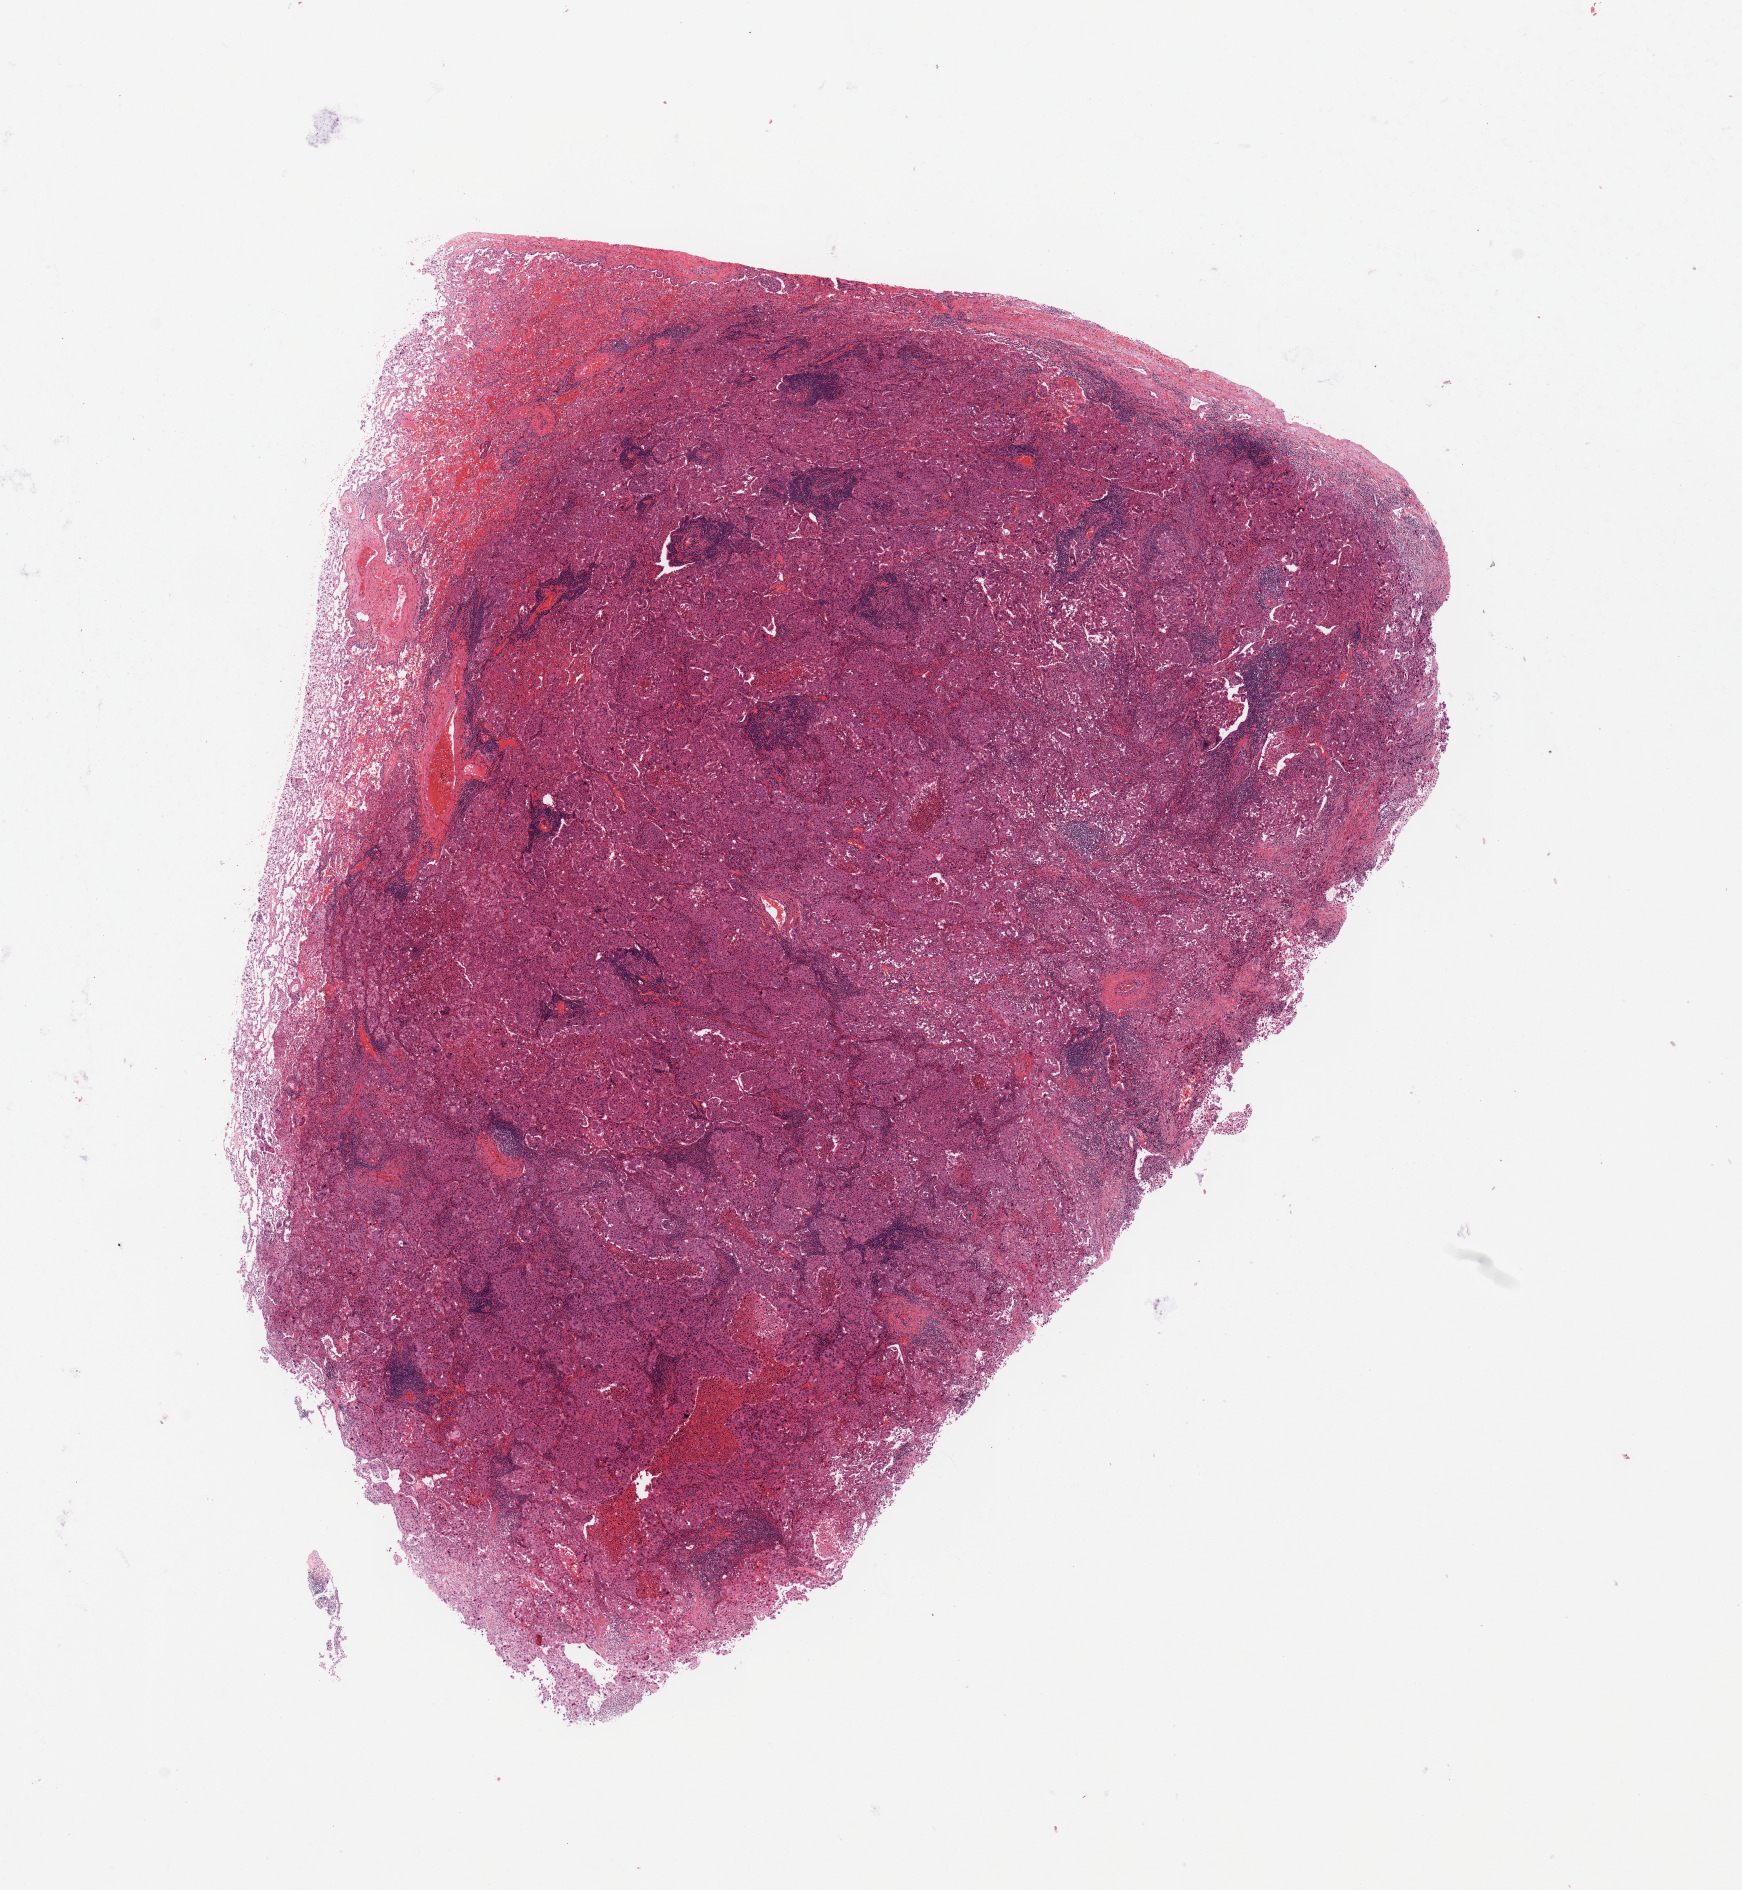
Digitized H&E-stained tissue section (whole slide), shown as a low-resolution overview of the whole scanned area (about 13.8 x 15.0 mm). Tumour tissue sample, sampled site: lung. Male, 56 y/o. Histologic grade: G3 (poorly differentiated). Pathologist review of this section (percent, as recorded): tumour nuclei 70%, necrosis 5%.
- AJCC pathologic stage: IIIA
- primary tumour site (as recorded): right lower lobe
- histologic diagnosis: Adenocarcinoma, NOS